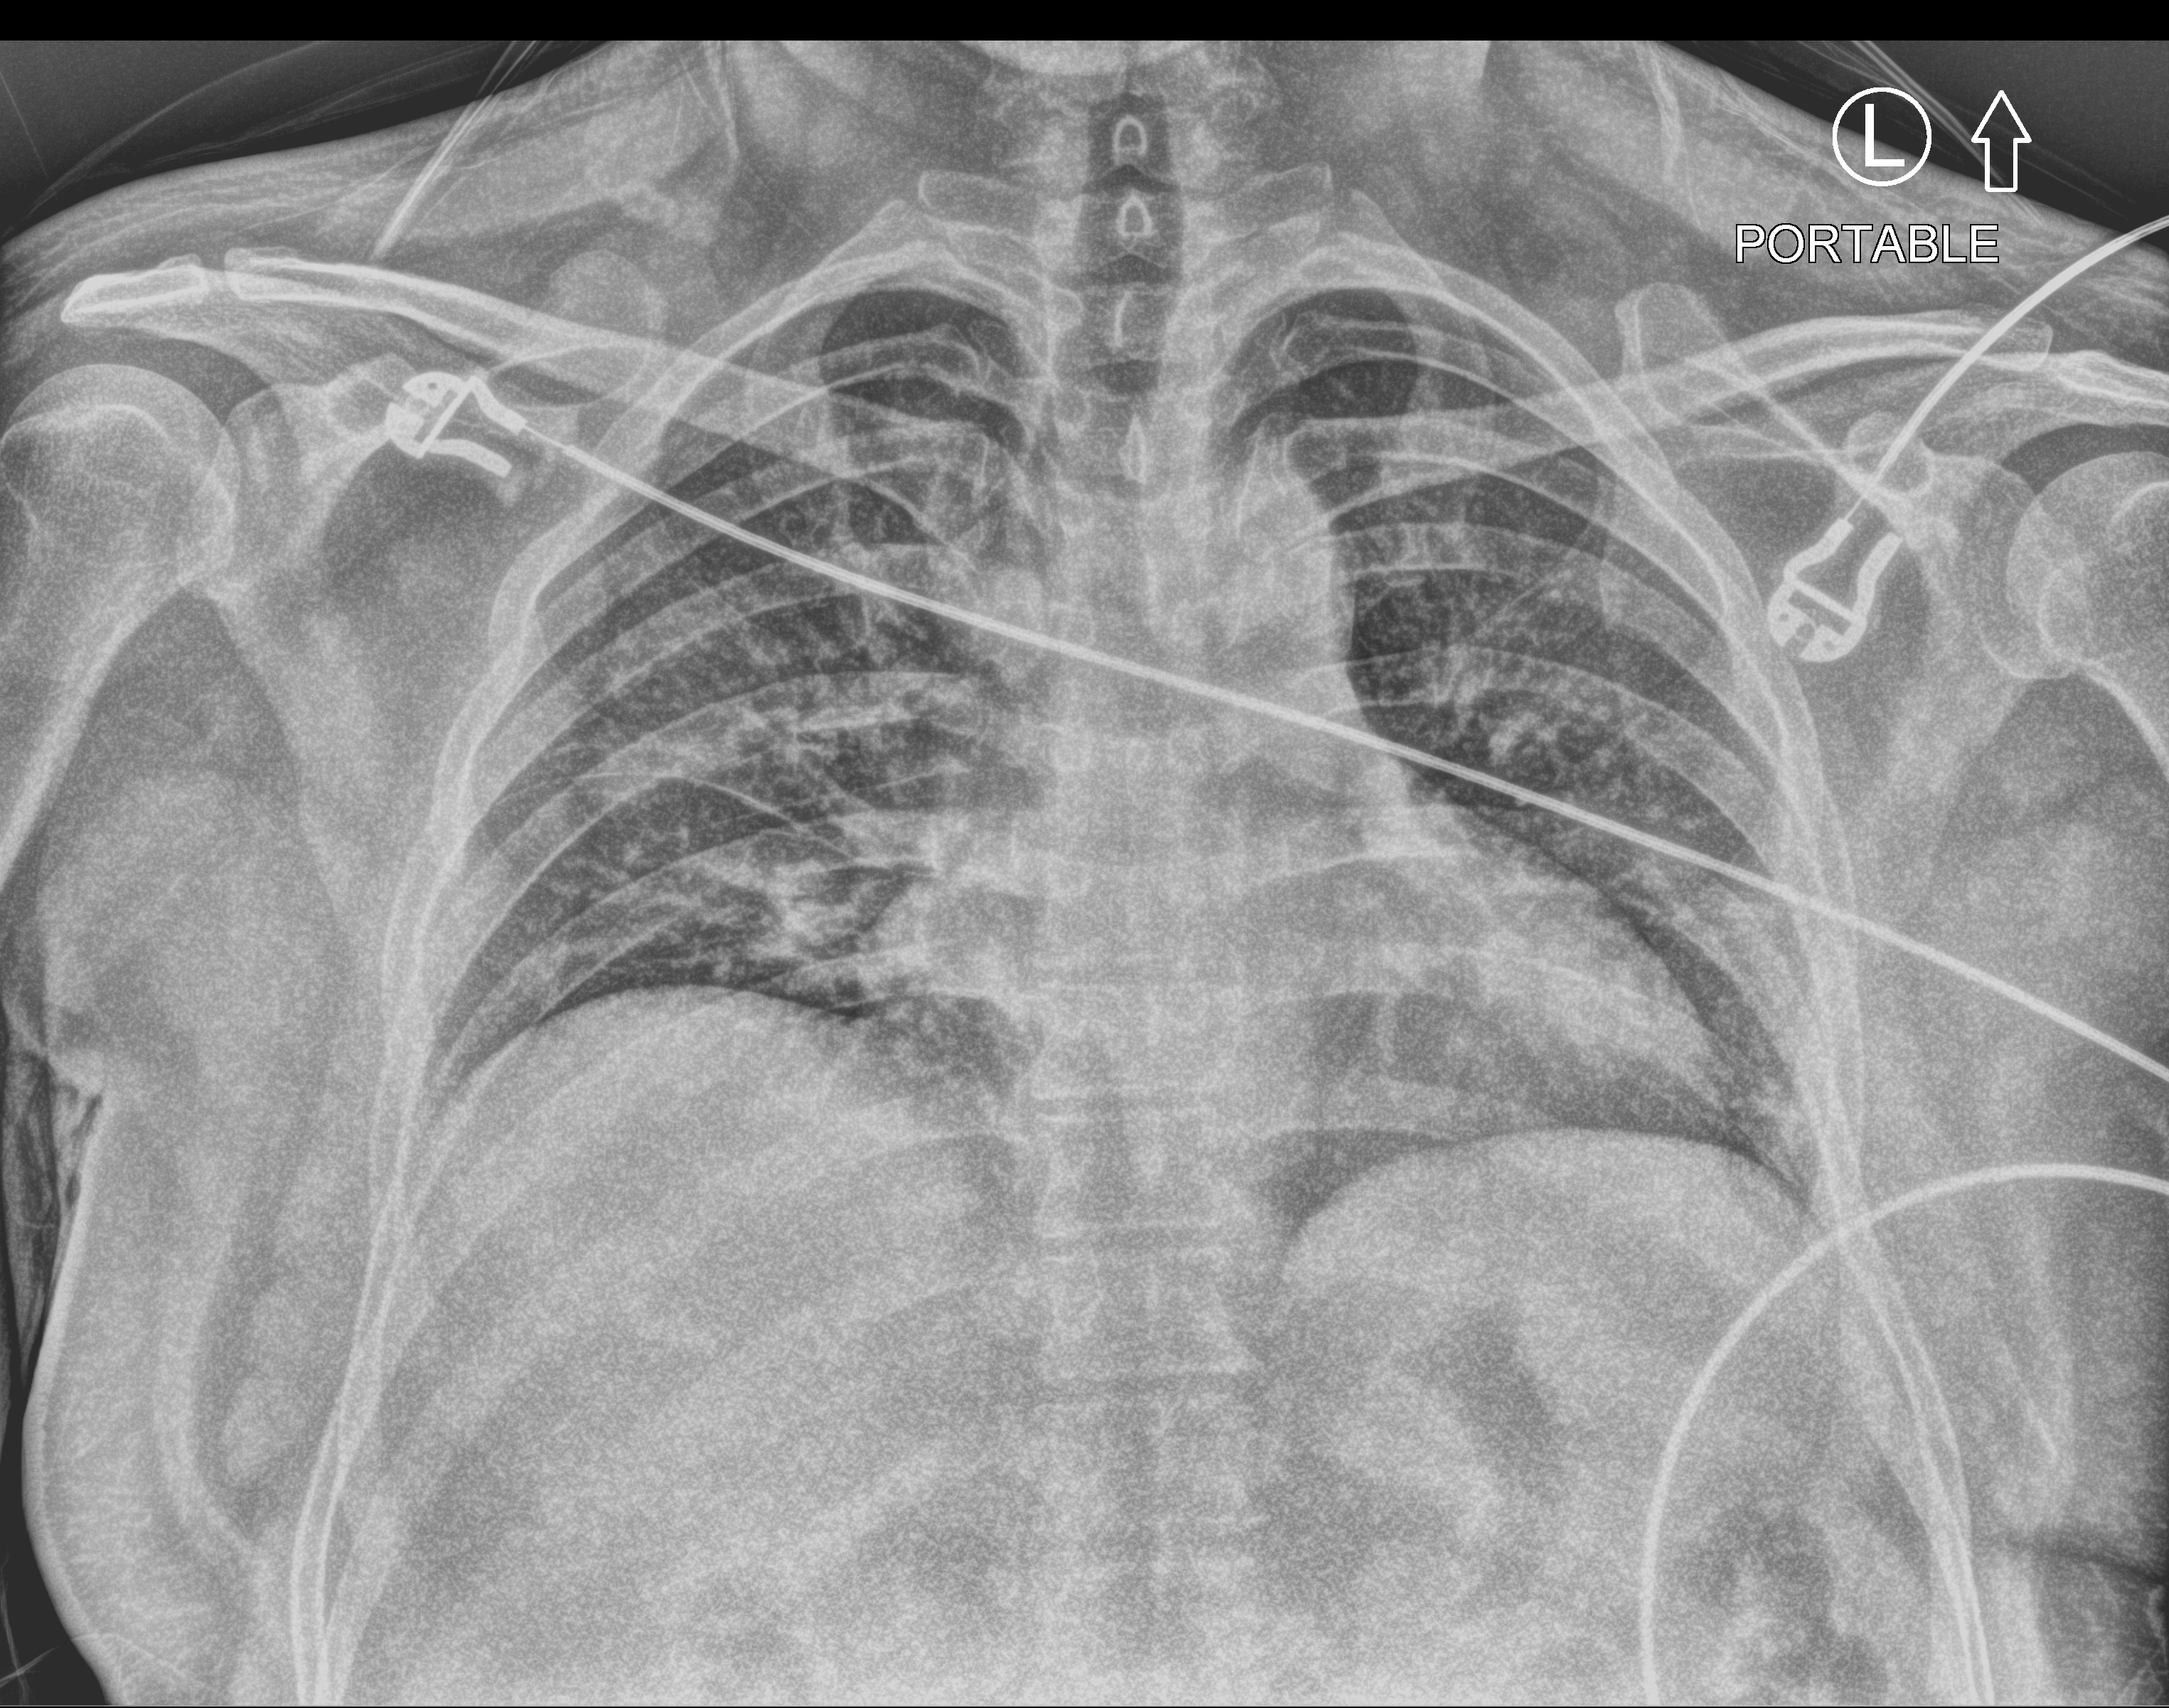
Bedside chest radiograph (computed radiography), anteroposterior (AP) projection. Male patient hospitalised with COVID-19, age 18–59 years.
Admission-level facts for this patient (not findings on this image; timing relative to this image not recorded):
- mechanically ventilated during this hospital stay: no
- other chronic lung disease (admission record): no